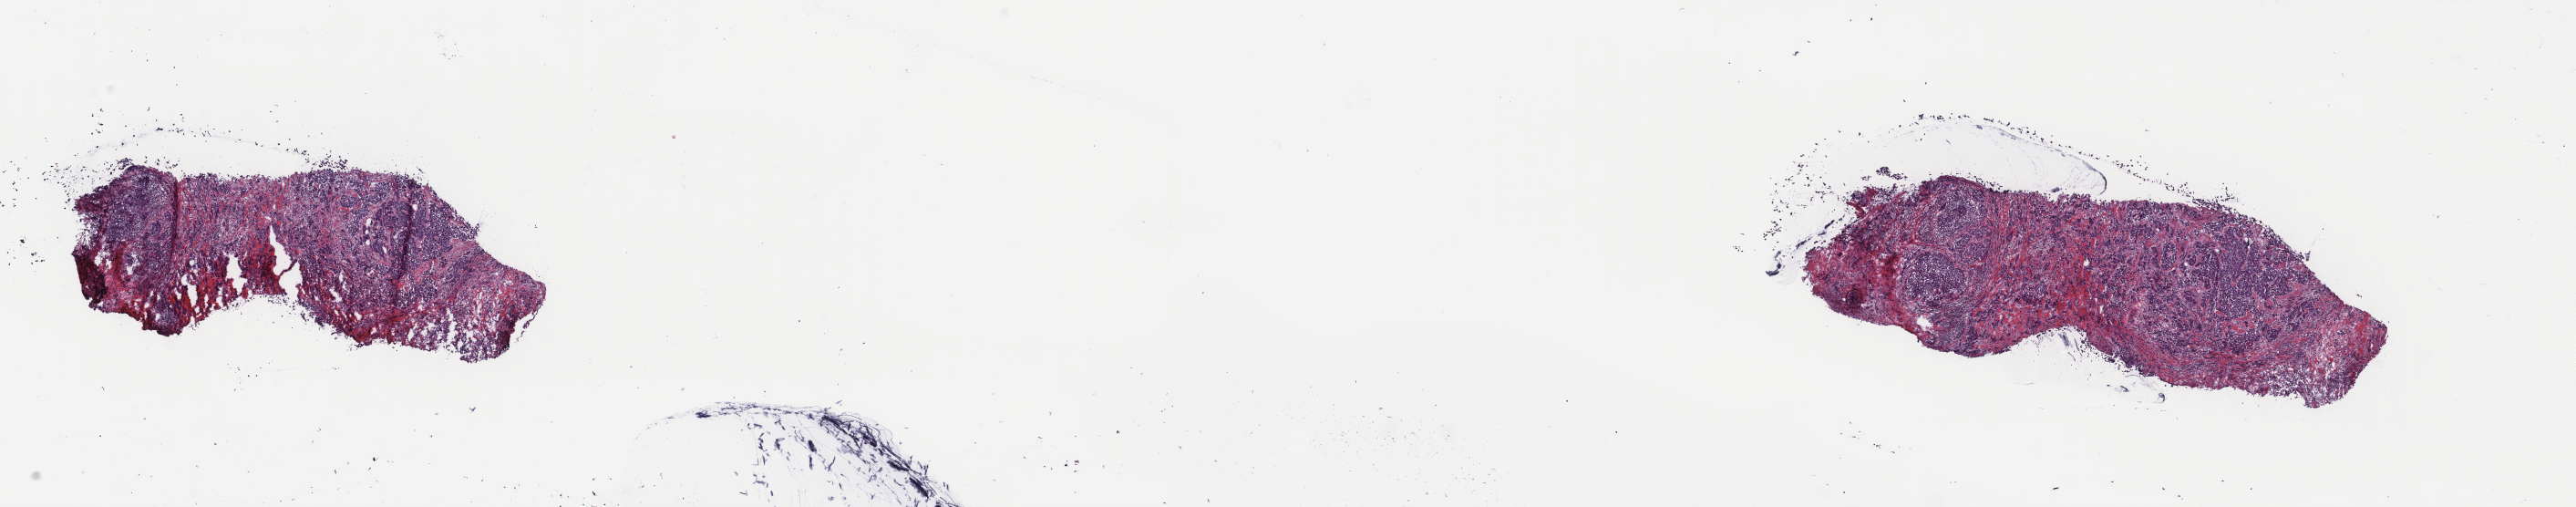
Whole-slide histology image, Hematoxylin and eosin (H&E) stained — whole scanned area (about 22.4 x 4.4 mm, slide scanned at 40x) shown as a low-resolution overview. Frozen section. Sample: primary tumour, breast. Patient: female, age at initial diagnosis 54 years. Composition of this section per pathologist review: tumour cells 90%, tumour nuclei 68%, normal cells 0%, stromal cells 10%, necrosis 0%. Infiltration values recorded for this section: lymphocyte infiltration 0%, monocyte infiltration 0%, neutrophil infiltration 0%.
Pathologic diagnosis: Infiltrating duct carcinoma, NOS. AJCC pathologic stage: IIA (7th edition).